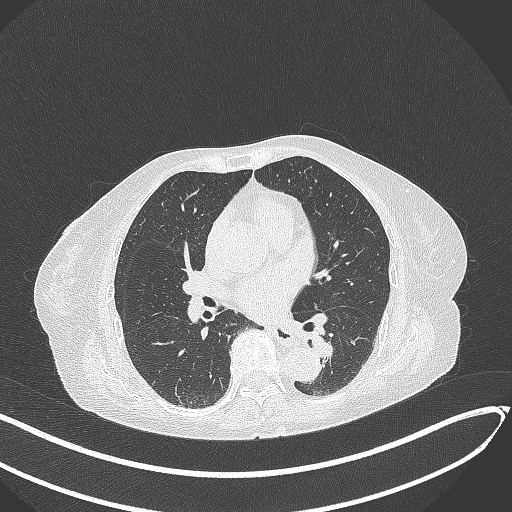
Chest CT, one axial slice; position 126 of 324 along the scan axis; reconstruction kernel B70f; 120 kVp; lung window (W 1500 / L -600 HU); 1 mm slice thickness; 512 × 512 image matrix, field of view 400 × 400 mm. Female patient, age 82 years. Case-level facts recorded for this patient, not image findings: clinical TNM (as recorded): T1b N0 M1.
Outlined on this slice (rectangle marked by the reading radiologist):
- lung tumour (recorded histology: adenocarcinoma): bounding box [x1, y1, x2, y2] px = [312, 329, 340, 361]